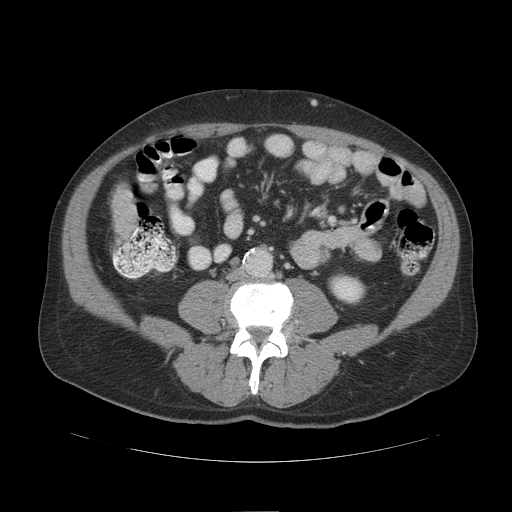
Contrast-enhanced abdominal CT (liver protocol), one axial slice; slice 21 of 109 in the series (ordered by position); reconstruction kernel STANDARD; soft-tissue window (W 400 / L 40 HU); 2.5 mm slice thickness; 512 × 512 image matrix. Case-level facts recorded for this patient, not image findings: diagnosis: hepatocellular carcinoma (patient treated with transarterial chemoembolisation; whether this scan precedes or follows treatment is not stated here); TNM stage (as recorded): Stage-IIIB; Child-Pugh class: A; tumour differentiation: poorly differentiated; tumour nodularity: multinodular.
Structures marked on this image (semi-automatic segmentation, software-assisted and operator-edited):
- liver parenchyma outside the tumour (the mass and vessels are separate outlines, so this box may not span the whole liver): bounding box <112,187,138,242> (left, top, right, bottom; pixels)
- liver vessels: <133,232,136,236>